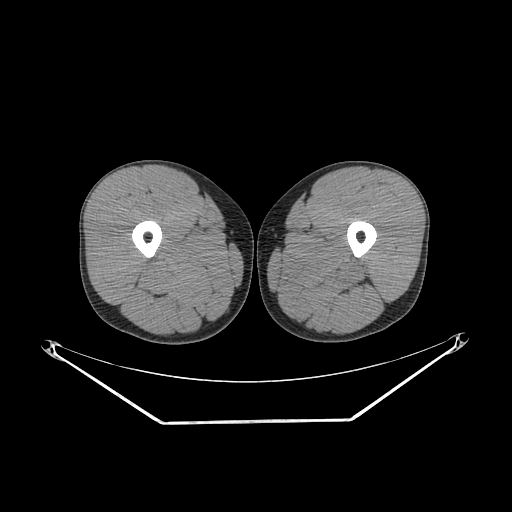
CT of an extremity soft-tissue mass (from a PET/CT study), one axial slice. Position 233 of 267 along the scan axis. Reconstruction kernel SOFT. Soft-tissue window (W 400 / L 40 HU). 3.75 mm slice thickness. 512 × 512 image matrix, field of view 500 × 500 mm. Male patient. From the clinical record (not read from this slice): histological type: extraskeletal osteosarcoma; grade: high; site of the primary tumour: left adductur.
Outlined on this slice (expert contour drawn on MRI and transferred to this co-registered scan by the dataset authors):
- gross tumour volume (mass): box from (x=276, y=242) to (x=375, y=296) px